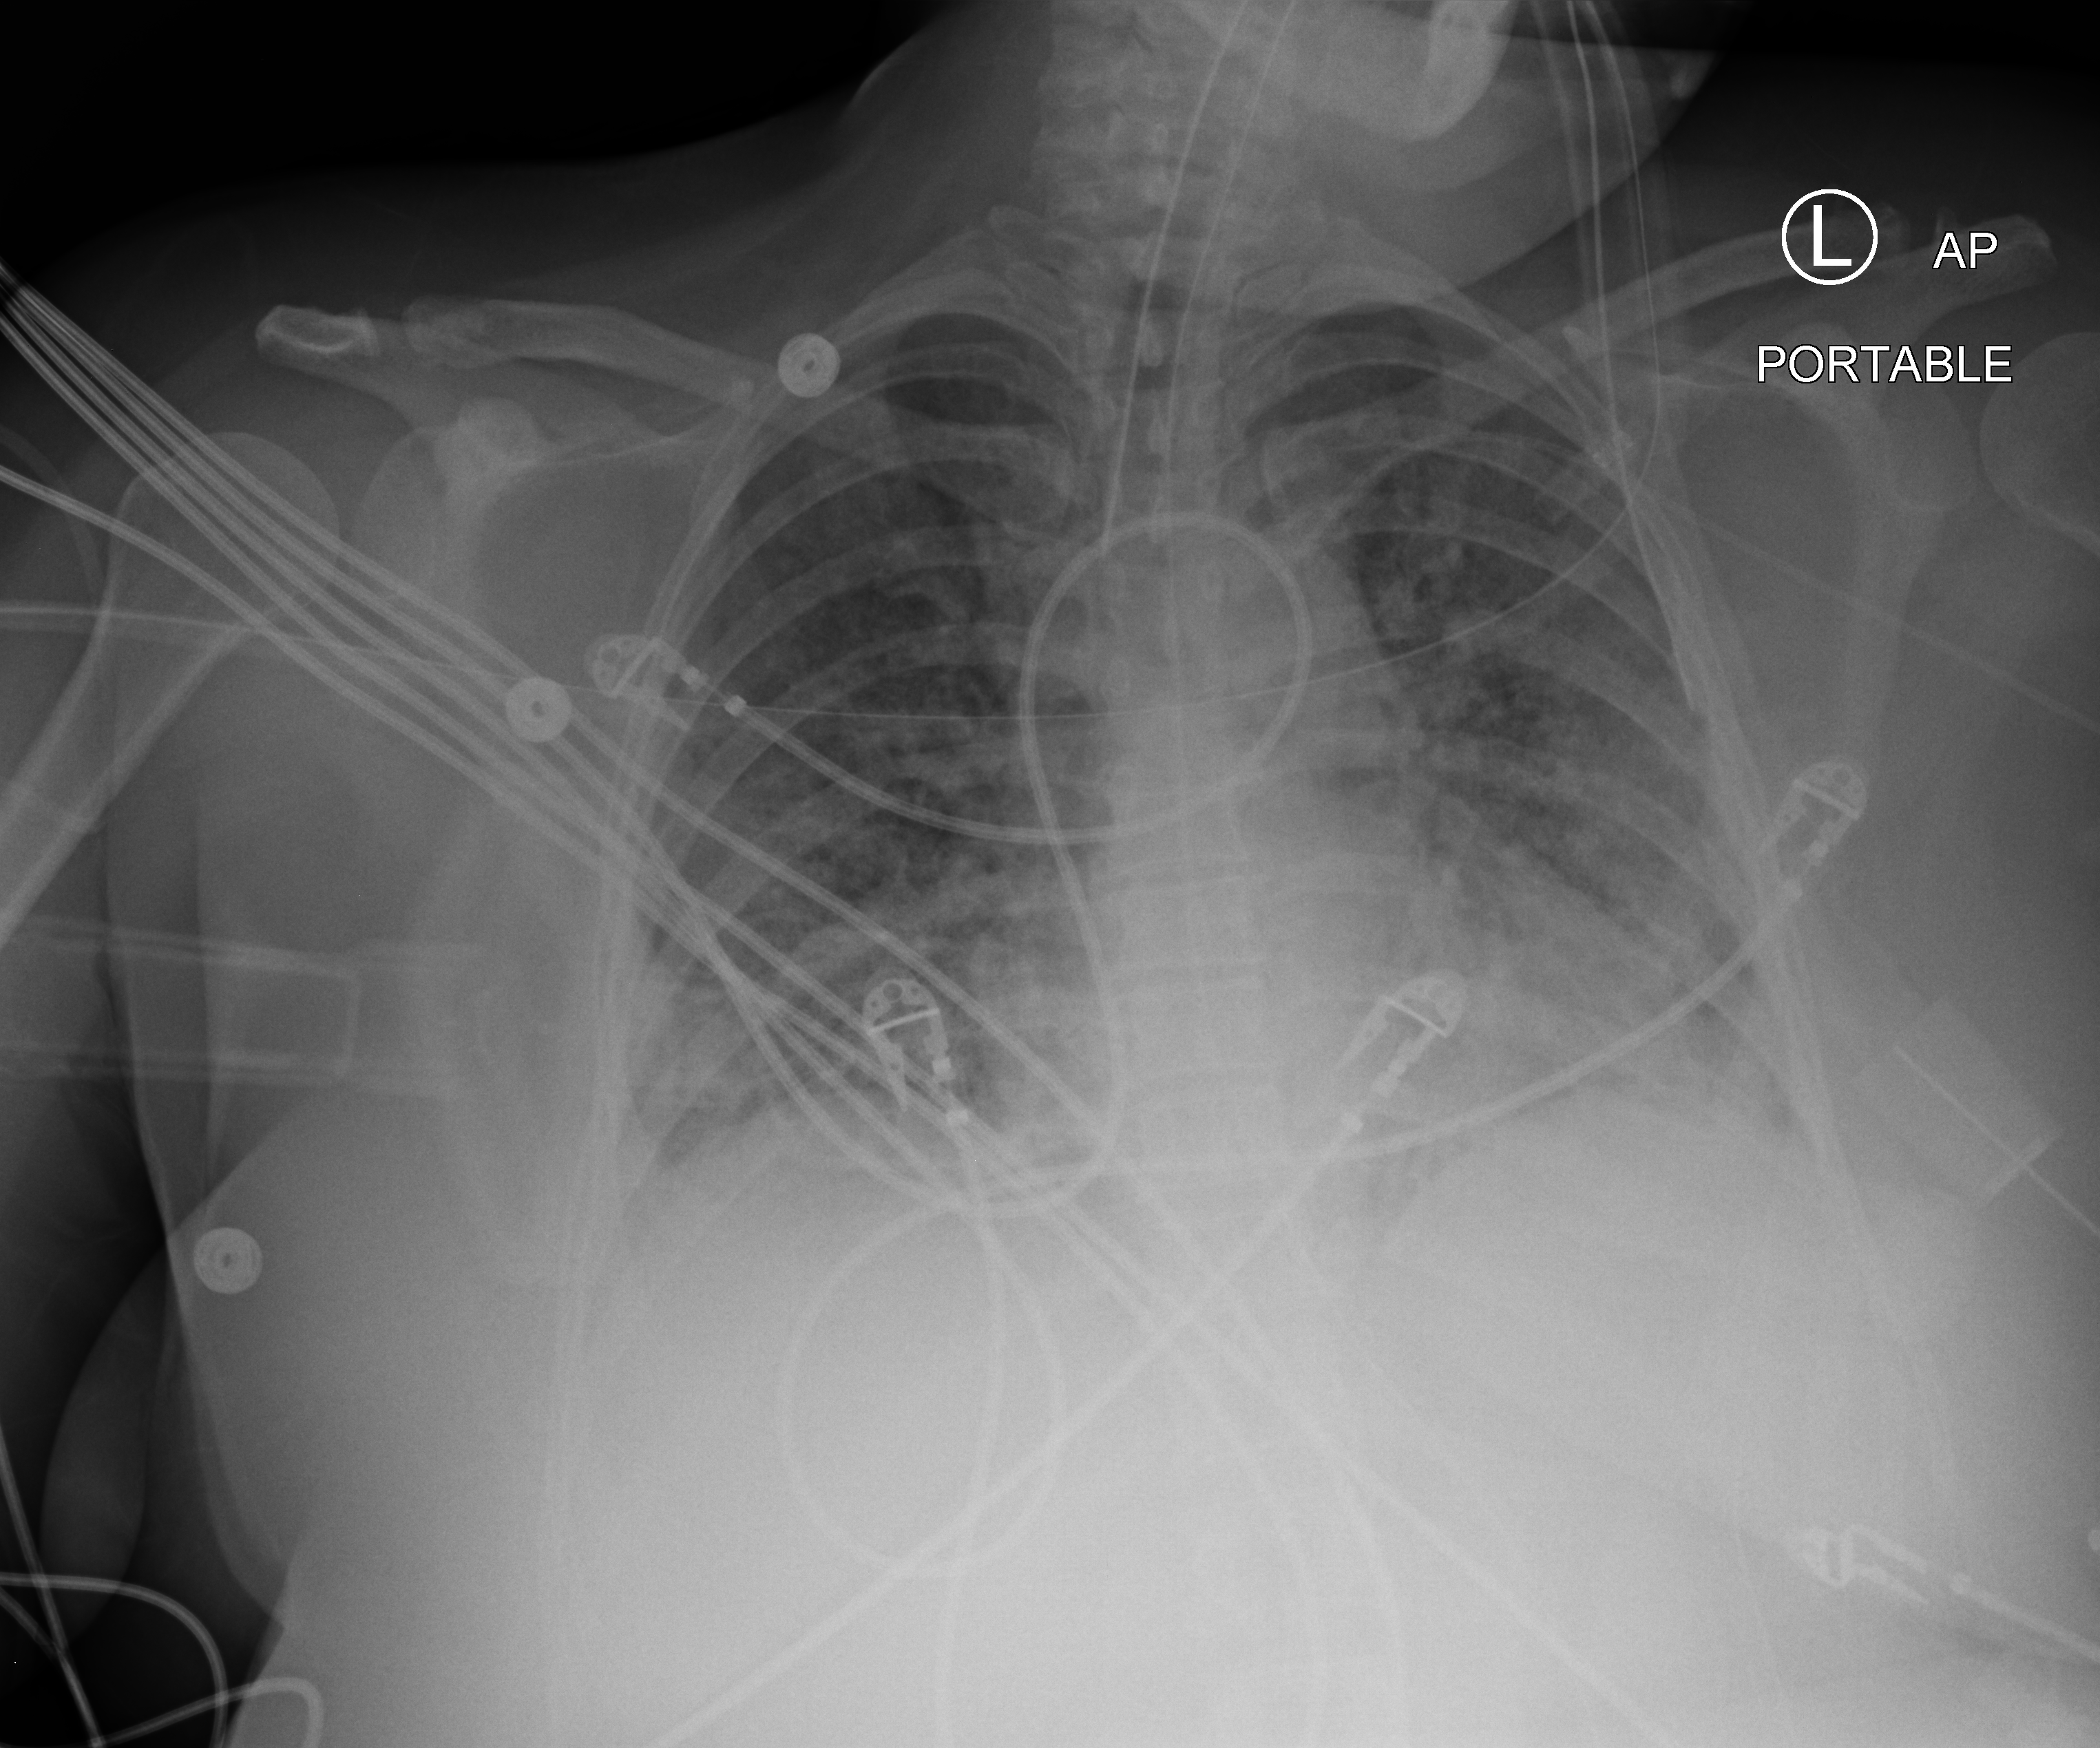
Chest X-ray (portable), anteroposterior (AP) projection. Female patient hospitalised with COVID-19, age 18–59 years.
Admission-level facts for this patient (not findings on this image; timing relative to this image not recorded): mechanically ventilated during this hospital stay: yes; length of hospital stay: 95 days; admitted to intensive care during this hospital stay: yes.